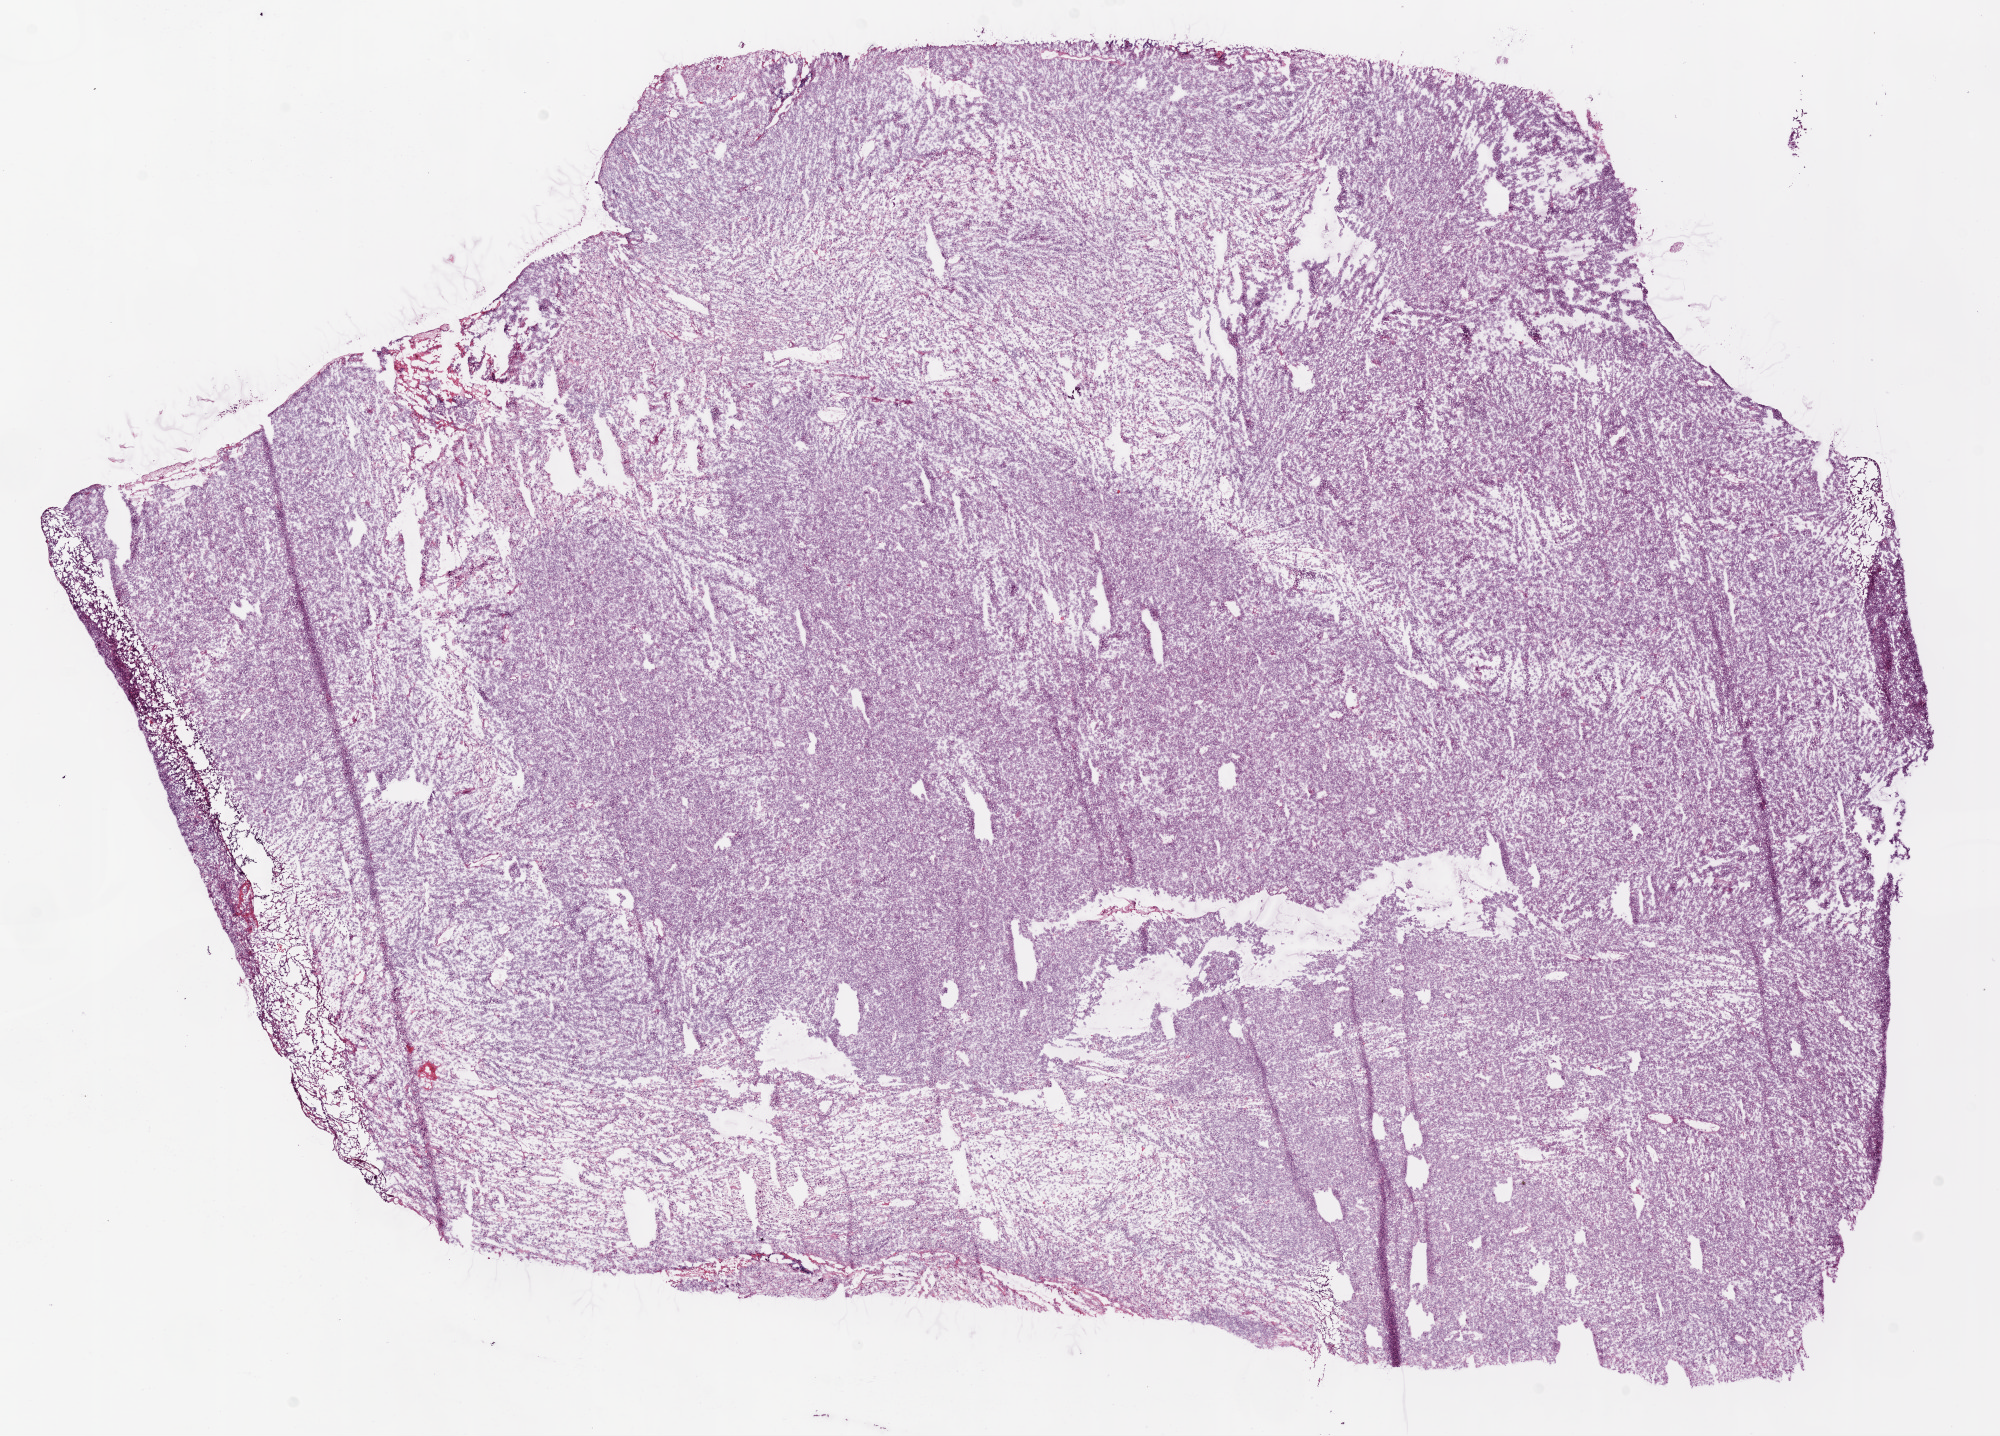
Hematoxylin and eosin (H&E) stained whole-slide image, whole scanned area (about 16.0 x 11.5 mm, acquisition: 20x scan) shown as a low-resolution overview, frozen section, sample: primary tumour, ovary. Patient: female, age at initial diagnosis 74 years. Slide review estimates, as recorded: tumour cells 60%, tumour nuclei 85%.
Pathologic diagnosis: Serous cystadenocarcinoma, NOS.